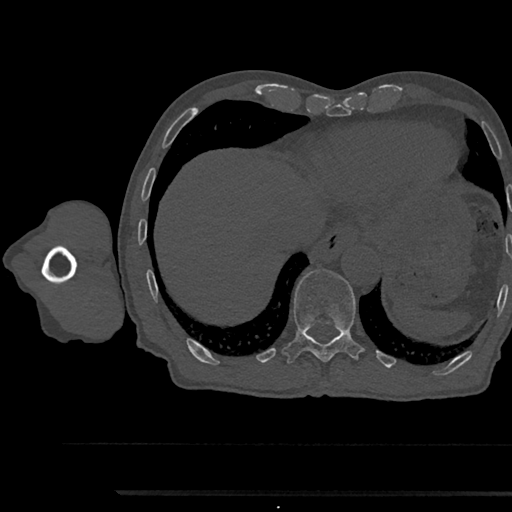
CT including the spine, one axial slice. Position 790 of 797 along the scan axis. Reconstruction kernel Br40s/3. Bone window (W 1800 / L 400 HU). 512 × 512 image matrix, field of view 367 × 367 mm. Male patient, age 79 years. Case-level facts recorded for this patient, not image findings: primary cancer: prostate.
Outlined on this slice (semi-automatically segmented with operator editing):
- T11 vertebra: box from (x=283, y=269) to (x=363, y=363) px